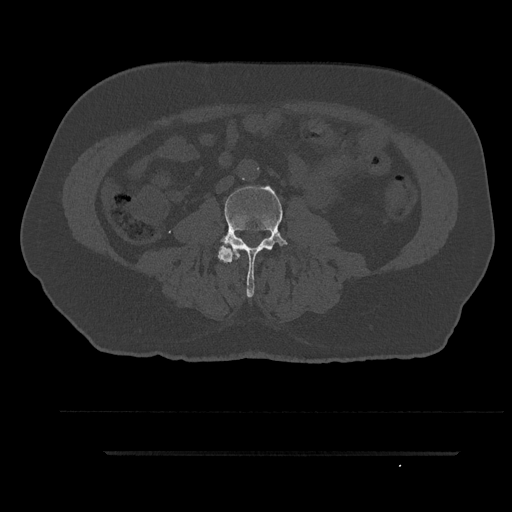
CT including the spine, one axial slice; position 37 of 797 along the scan axis; reconstruction kernel Br40s/3; bone window (W 1800 / L 400 HU); 0.5 mm slice thickness; 512 × 512 image matrix, field of view 432 × 432 mm. Male patient, age 63 years. Case-level facts recorded for this patient, not image findings: primary cancer: renal; vertebrae with lytic lesions (as recorded): T8.
Annotated regions visible in this slice (semi-automatically segmented with operator editing):
- L3 vertebra: bounding box [x1, y1, x2, y2] px = [217, 185, 288, 298]